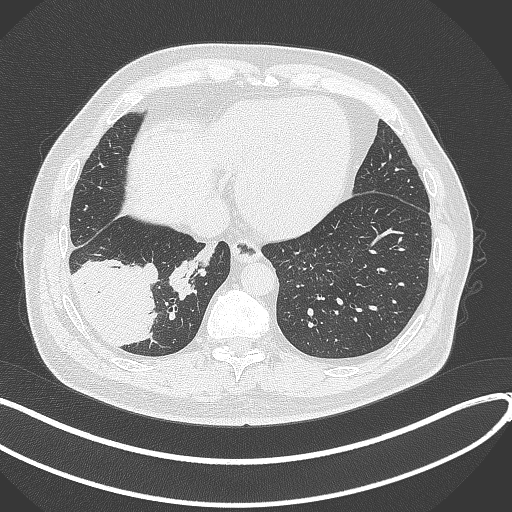
Chest CT, one axial slice. Slice 91 of 360 in the series (ordered by position). Reconstruction kernel B70f. 120 kVp. Lung window (W 1500 / L -600 HU). 1 mm slice thickness. 512 × 512 image matrix, field of view 400 × 400 mm. Male patient, age 59 years.
Annotated regions visible in this slice (bounding box drawn by a radiologist):
- lung tumour (recorded histology: adenocarcinoma): bounding box (x1, y1, x2, y2) in pixels: (66, 251, 161, 348)